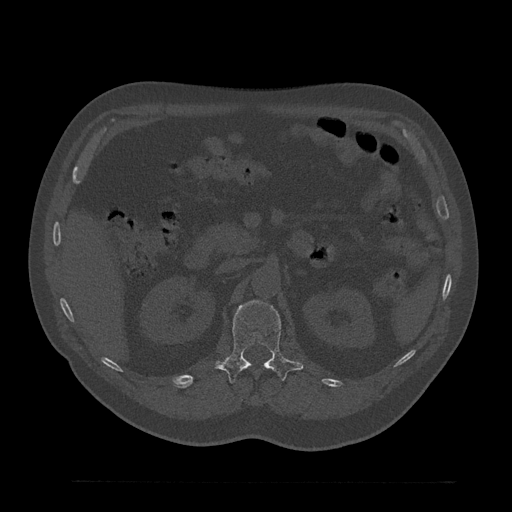
CT including the spine, one axial slice; position 174 of 797 along the scan axis; 120 kVp; bone window (W 1800 / L 400 HU); 0.5 mm slice thickness; 512 × 512 image matrix, field of view 430 × 430 mm. Patient: male, 61 years. From the clinical record (not read from this slice): primary cancer: prostate.
Annotated regions visible in this slice (semi-automatic segmentation, software-assisted and operator-edited):
- L1 vertebra: bounding box [x1, y1, x2, y2] px = [216, 300, 304, 384]